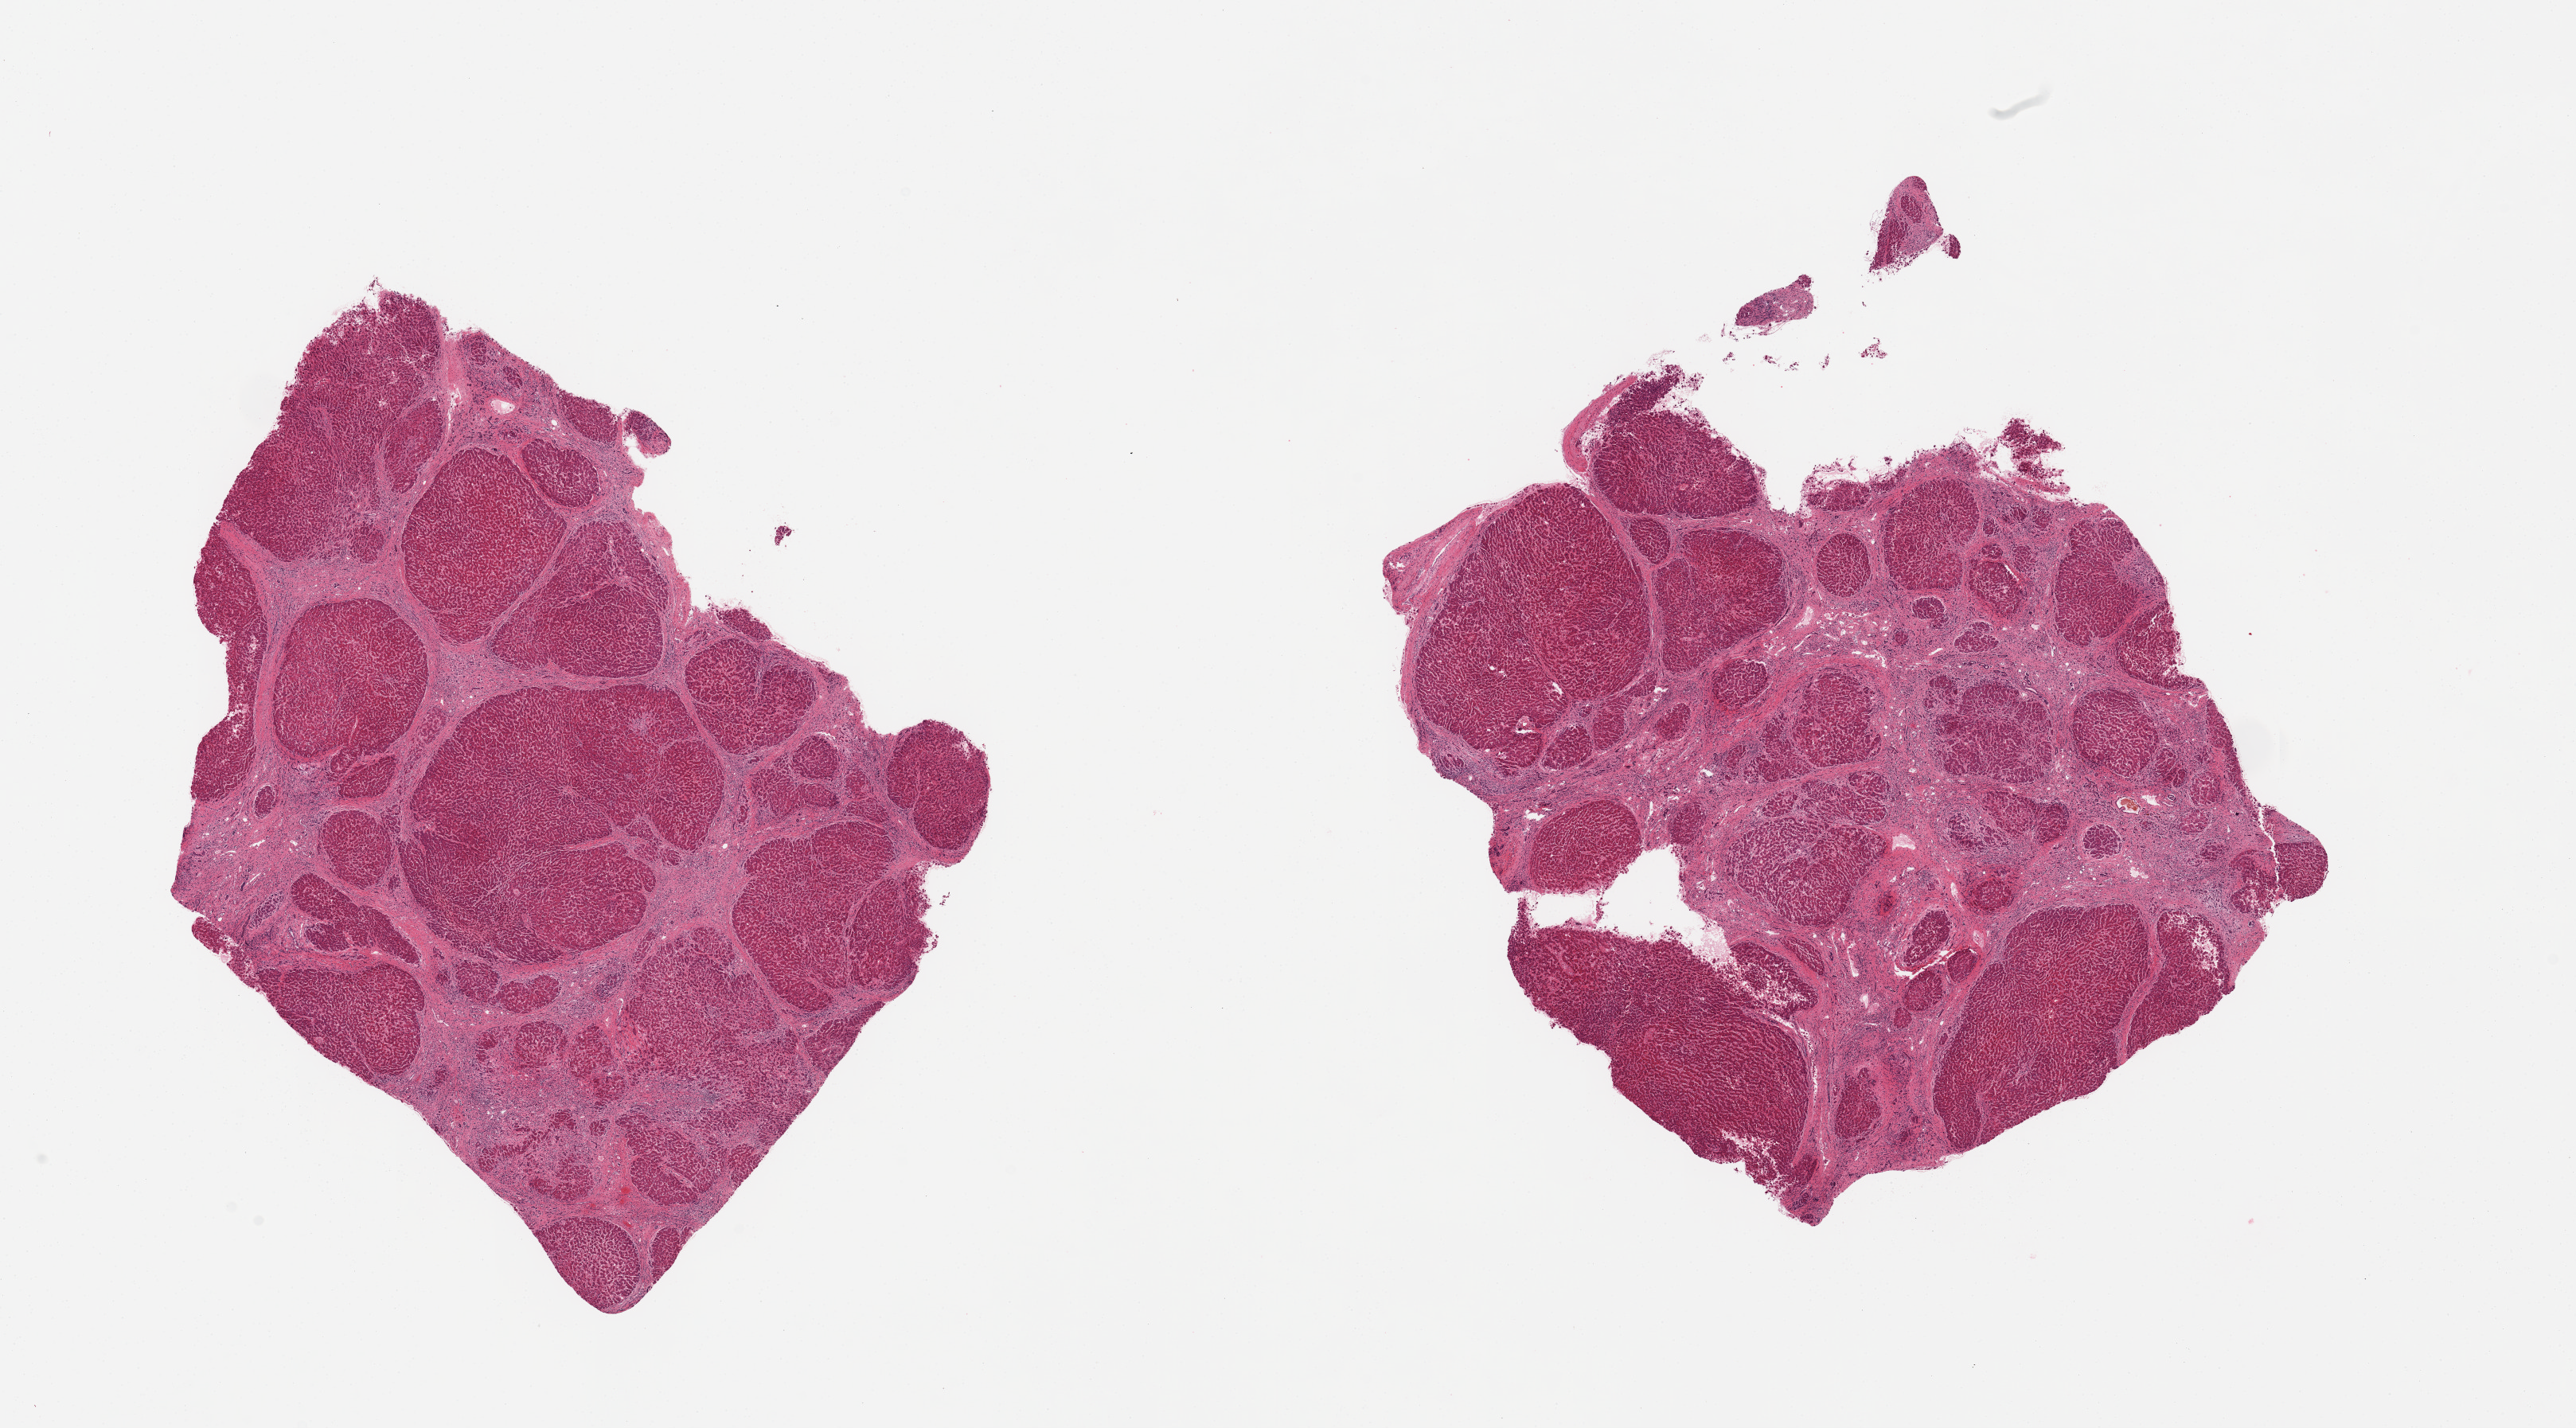
Whole-slide image, H&E stain, shown as a low-resolution overview of the whole scanned area (about 25.6 x 14.2 mm); PAXgene-fixed paraffin-embedded (PFPE) section; section of liver (target tissue); donor tissue sample.
Review note (as recorded): 2 pieces; nodular cirrhosis.